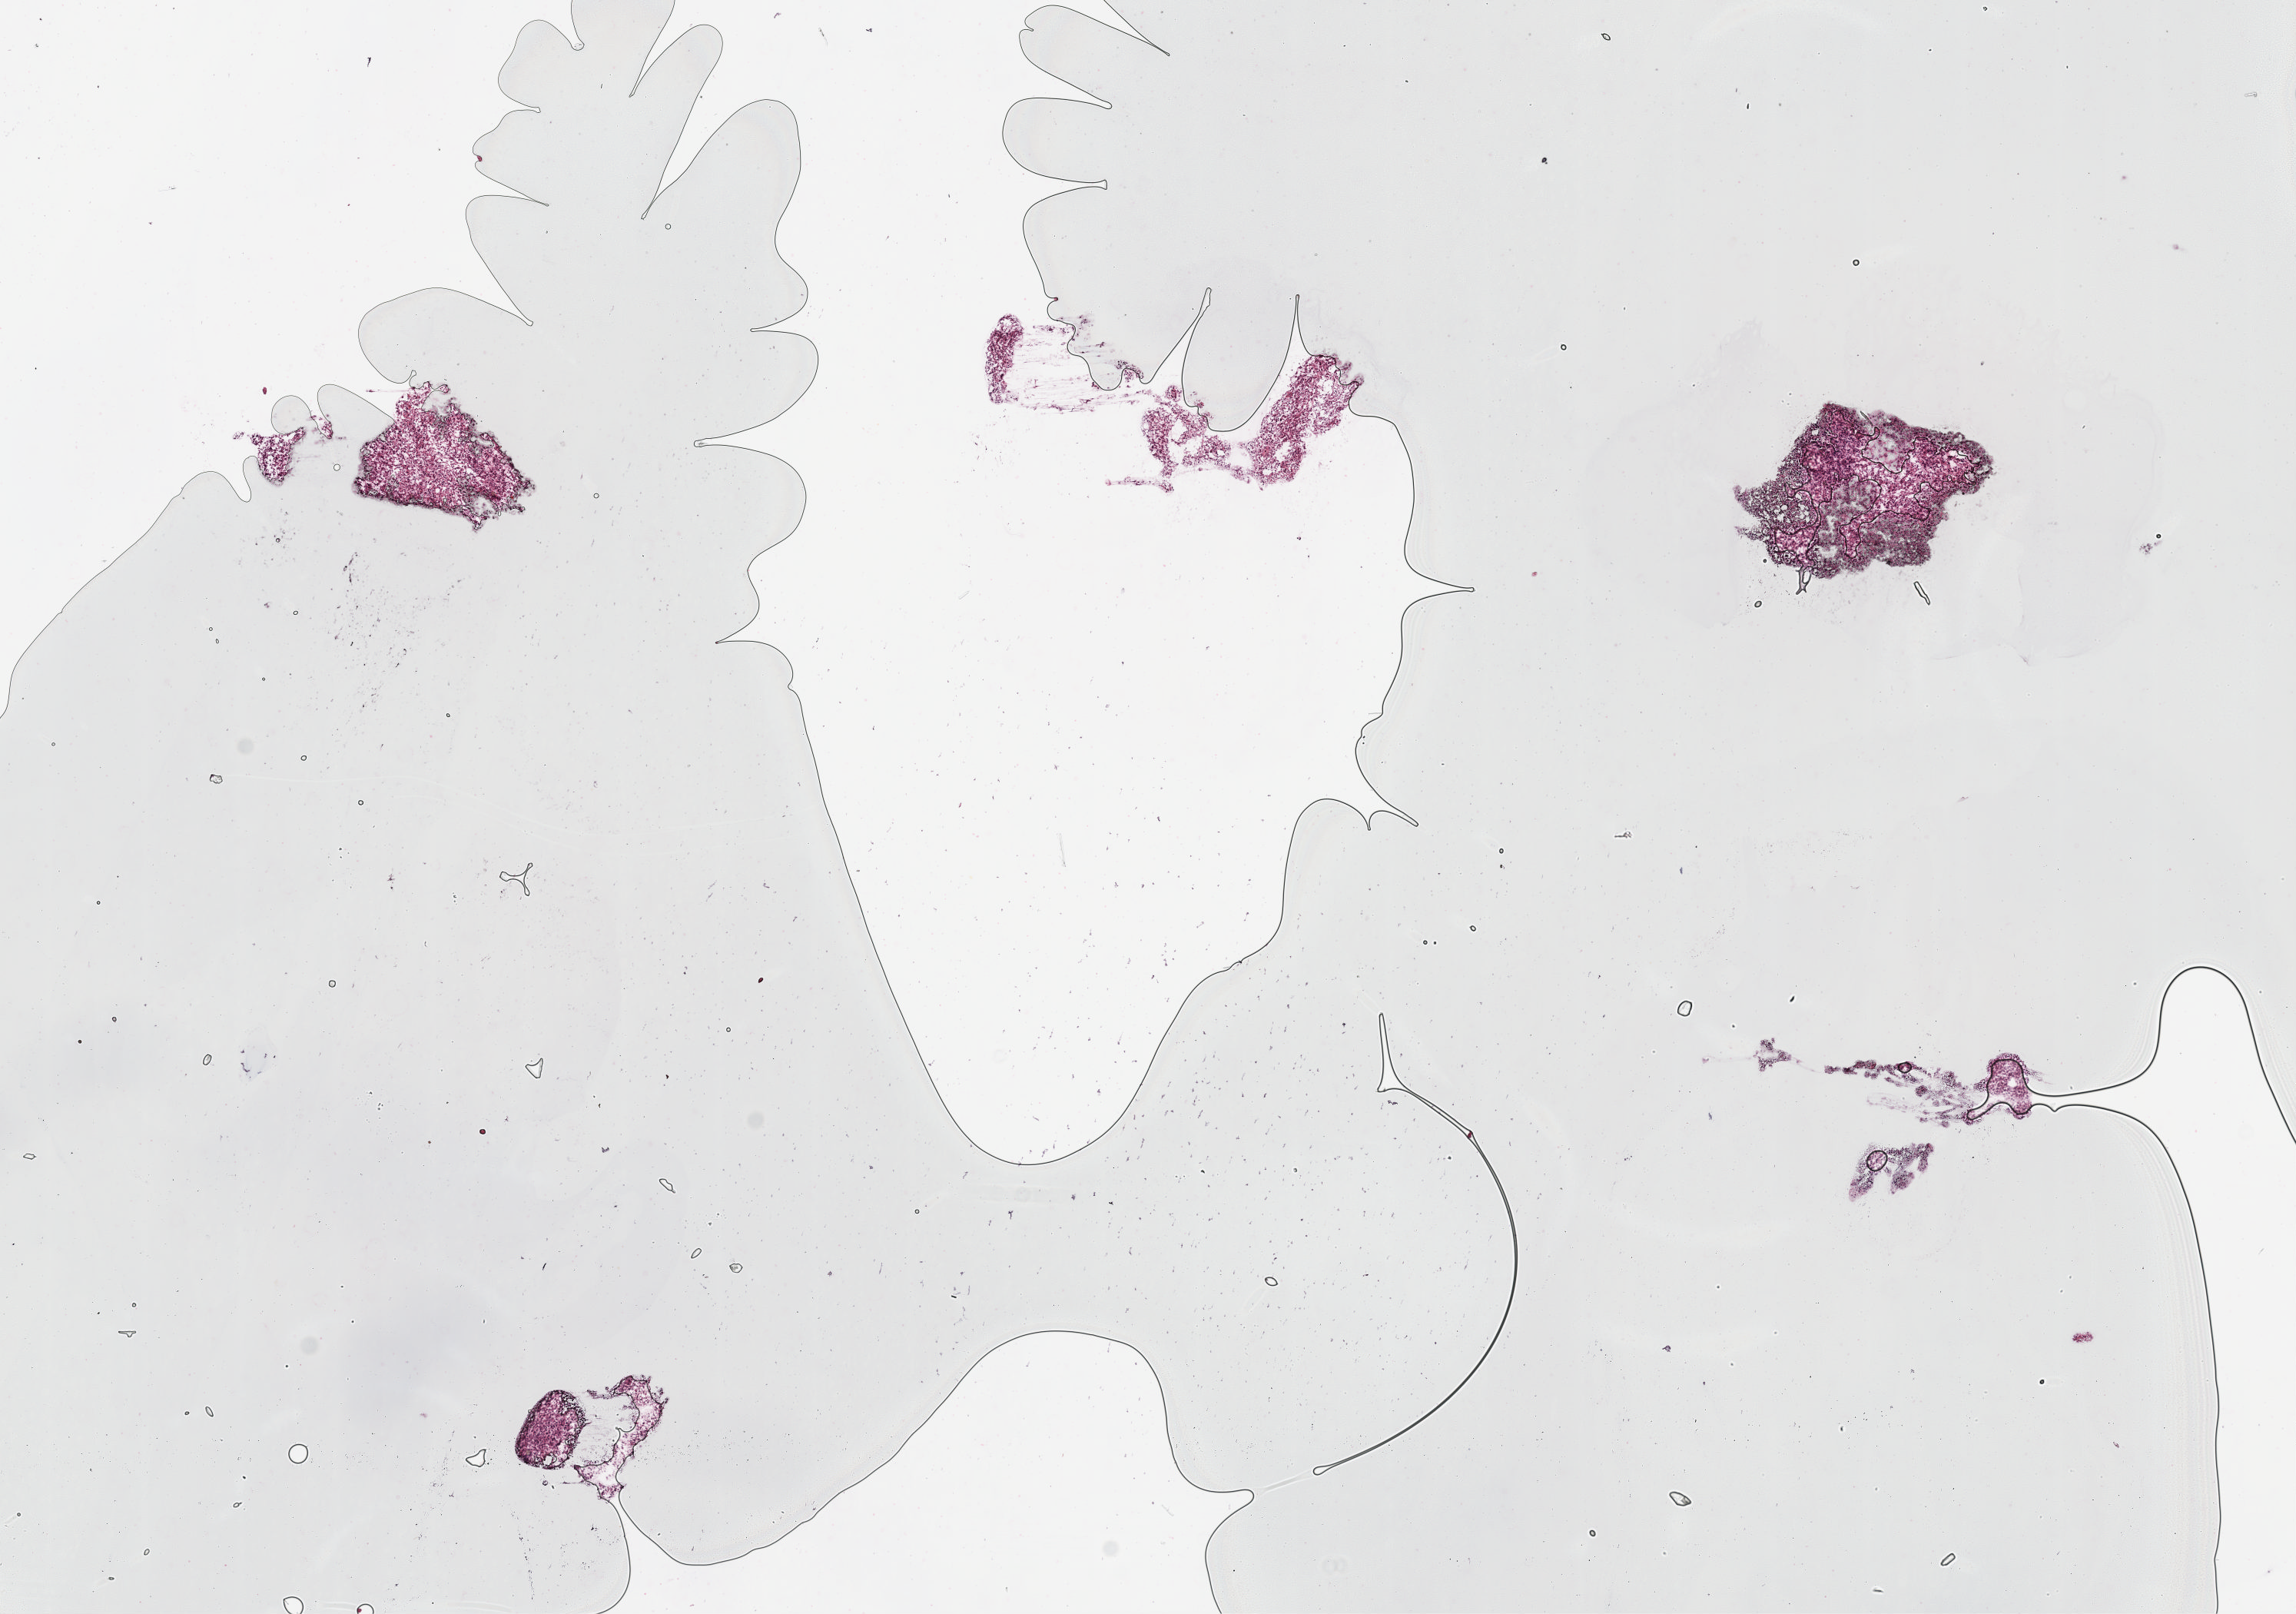
H&E whole-slide image, low-resolution overview of the scanned area, about 12.1 x 8.5 mm, frozen section from the top of the tissue portion, sample: primary tumour, adrenal gland. Patient: female, age at initial diagnosis 59 years. Composition of this section per pathologist review: tumour cells 90%, tumour nuclei 95%, normal cells 0%, stromal cells 10%, necrosis 0%. Inflammatory infiltration, as recorded: lymphocyte infiltration 0%, monocyte infiltration 0%, neutrophil infiltration 0%.
• histologic diagnosis: Pheochromocytoma, NOS
• lymph nodes positive (case pathology): 0 of 1 examined